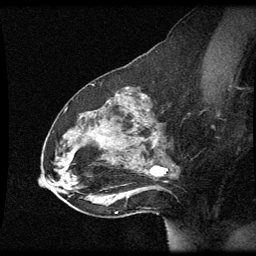
Breast MRI (dynamic contrast-enhanced), one sagittal slice. Dynamic contrast-enhanced series, image 2 of 3 at this slice position (ordered by acquisition). 1.5 T. TE 4.2 ms, TR 8.9 ms. 256 × 256 image matrix, field of view 200 × 200 mm. Female patient, age 49 years. Case-level facts recorded for this patient, not image findings: setting: breast cancer imaged before/during neoadjuvant chemotherapy; receptor status: HR-positive, HER2-negative.
Annotated regions visible in this slice (semi-automatic segmentation, software-assisted and operator-edited):
- analysis volume of interest (the breast-tissue region the enhancement analysis was run in; not a lesion): bounding box <46,92,177,205> (left, top, right, bottom; pixels)
- tumour enhancement mask (voxels above the 70 % enhancement threshold inside the analysis volume of interest): <151,142,156,173>